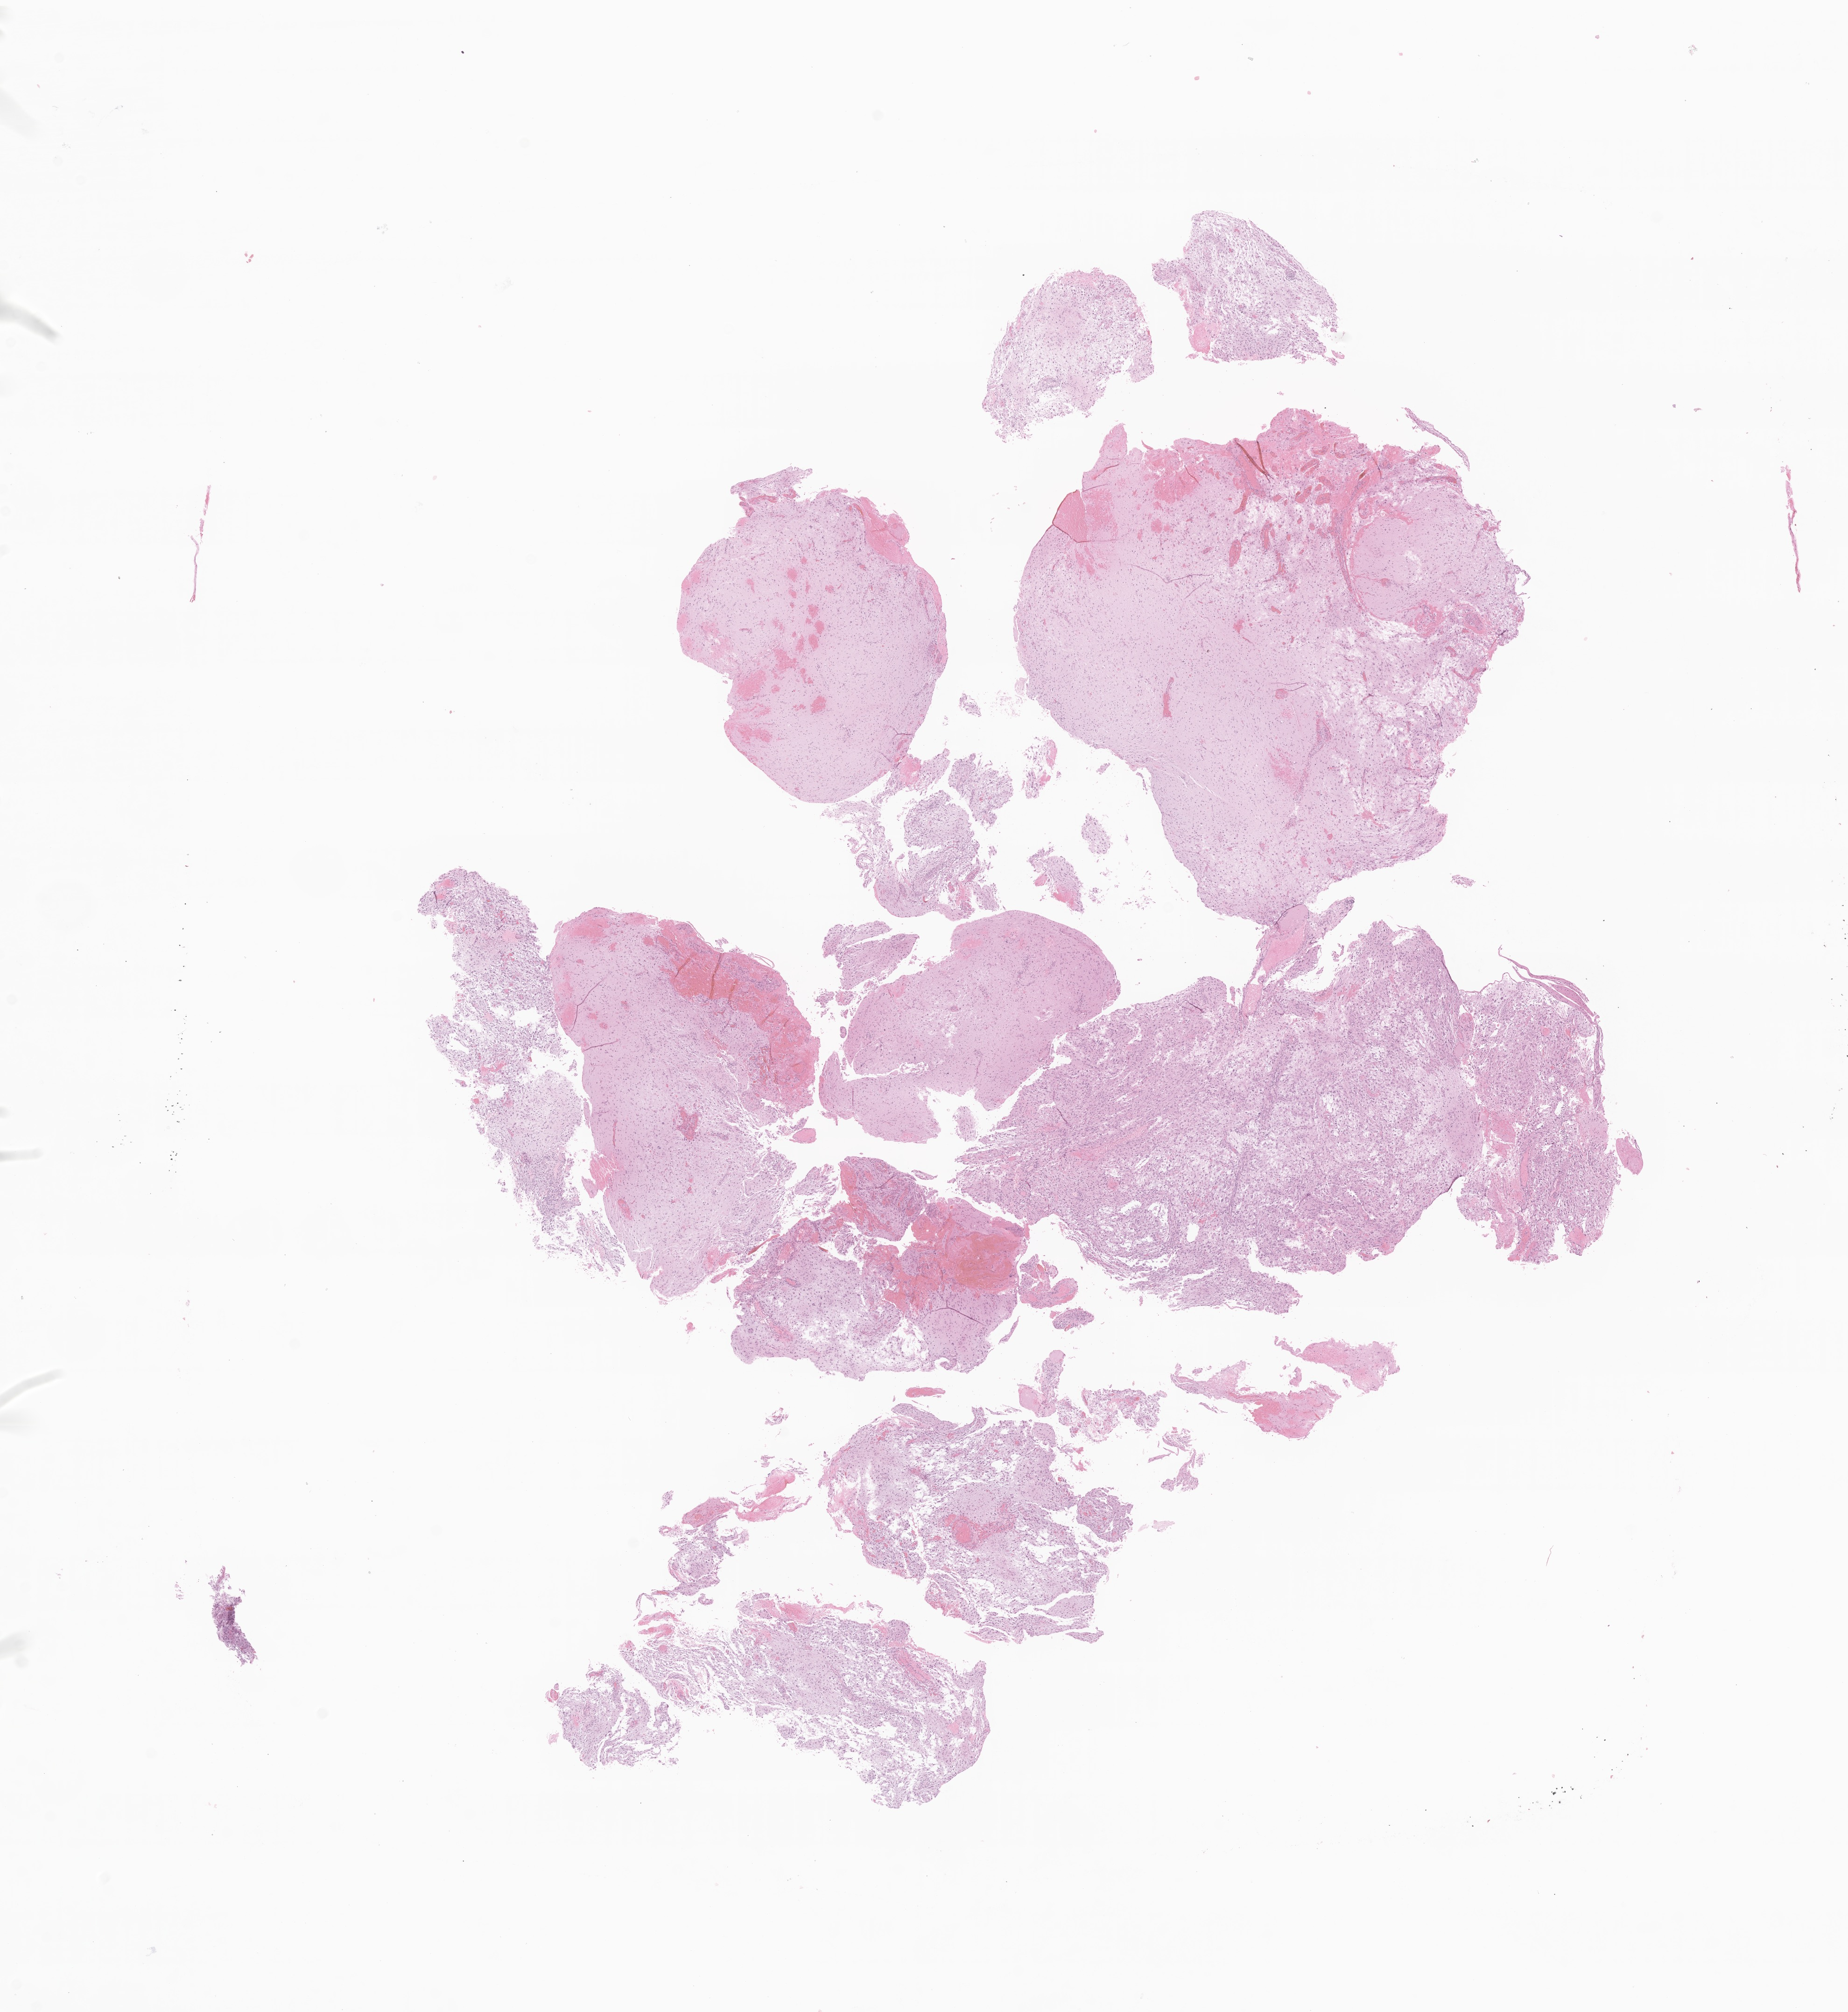
Digitized hematoxylin and eosin (H&E)-stained section of tumor tissue from the brain — a low-resolution overview of the entire scanned area, about 16.7 x 18.2 mm. FFPE section. Male patient, age 186 months.
Diagnosis: Astrocytoma, NOS.